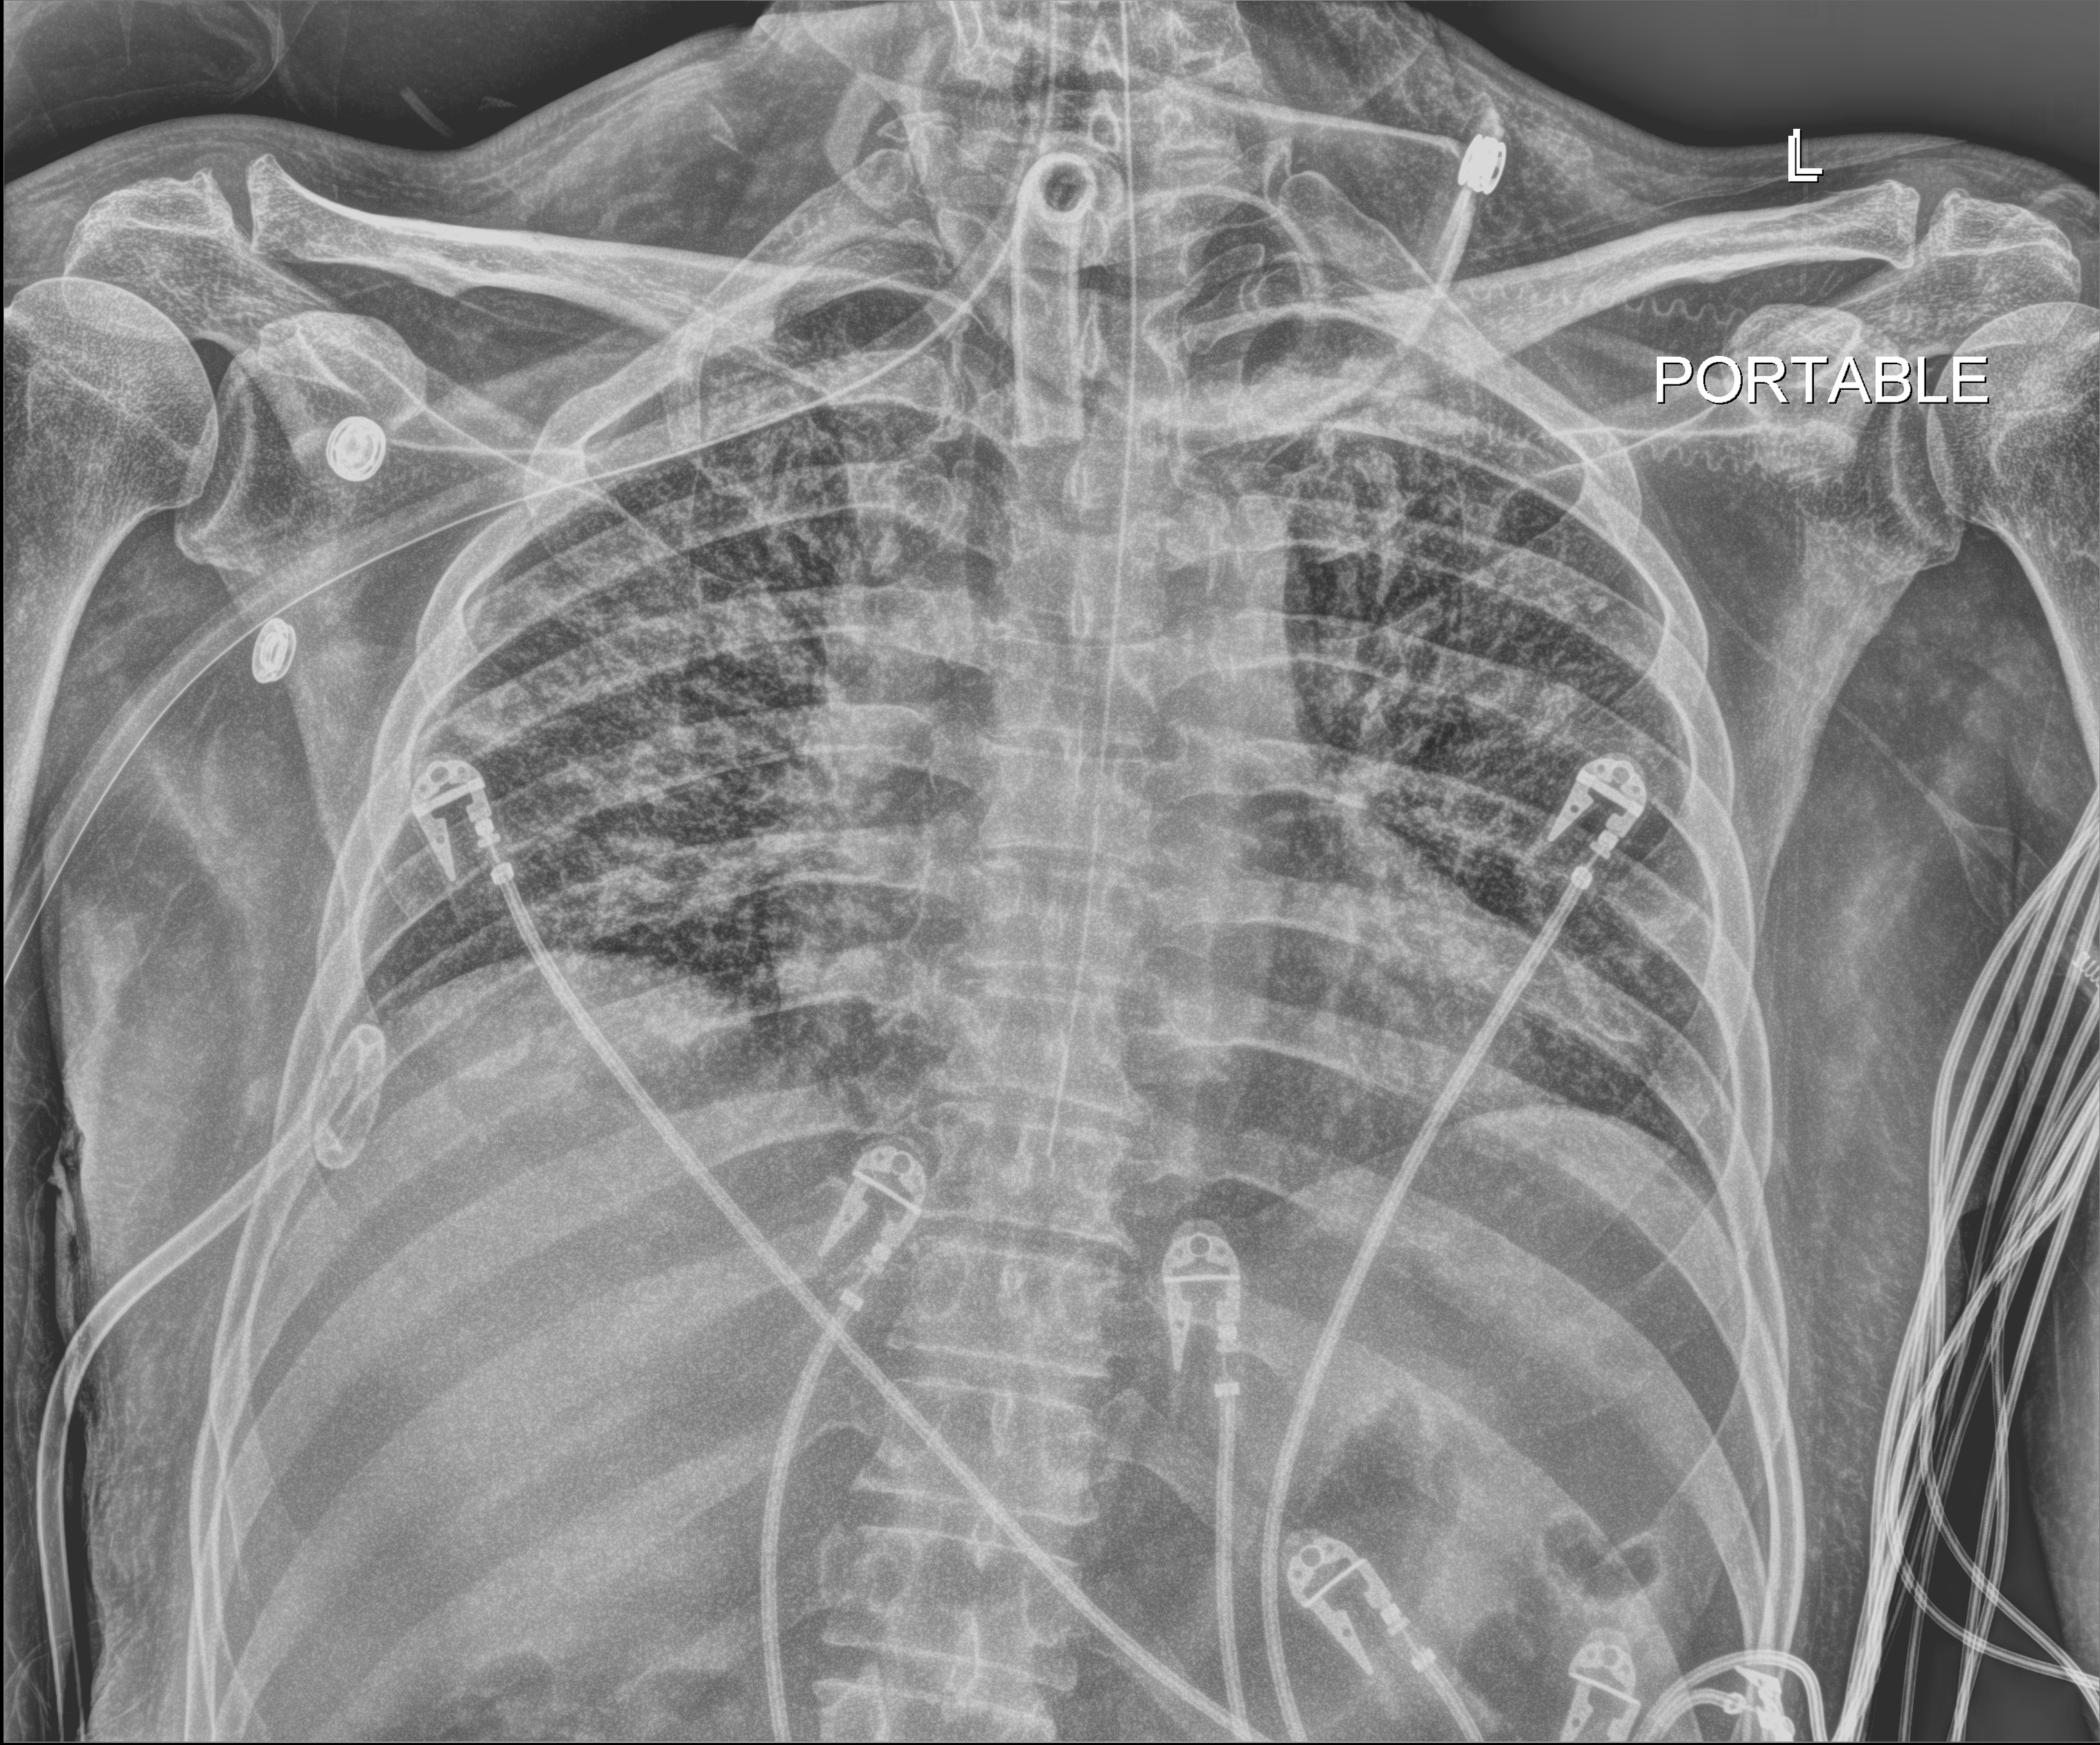
Chest X-ray (portable), anteroposterior (AP) projection. Male patient hospitalised with COVID-19, age 18–59 years.
Hospital-stay facts (about this admission, not read from this image; timing relative to this image not recorded):
- other chronic lung disease (admission record): no
- admitted to intensive care during this hospital stay: yes
- mechanically ventilated during this hospital stay: yes